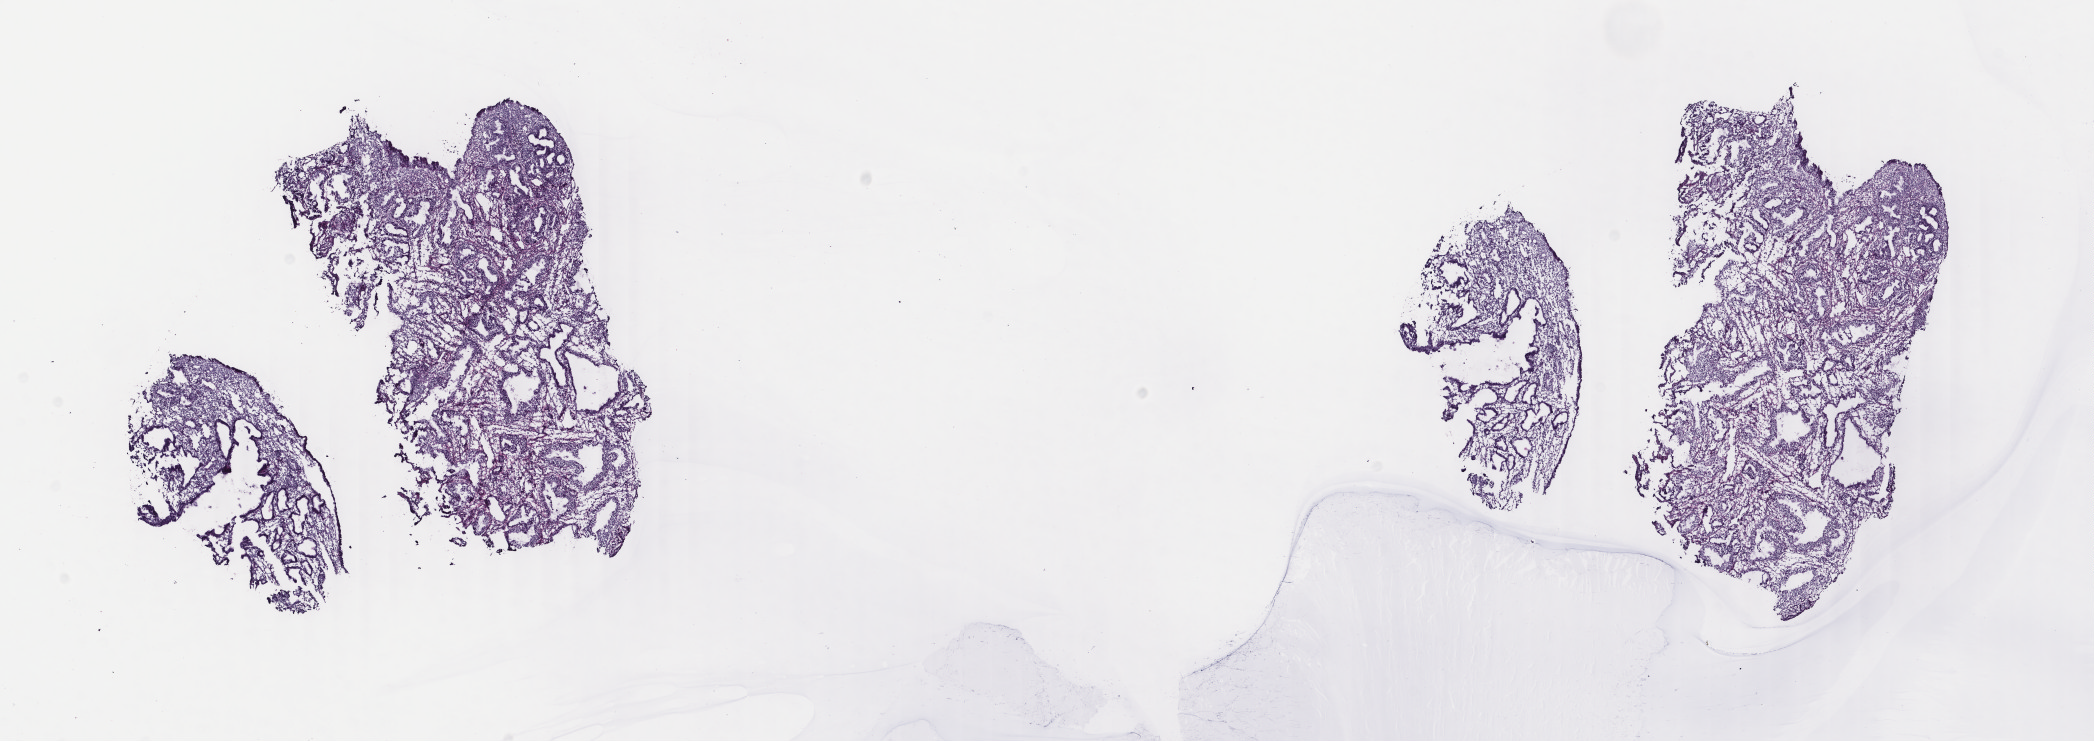
Digitized Hematoxylin and eosin (H&E) stained tissue section (whole slide), whole scanned area (about 16.7 x 5.9 mm, acquisition: 40x scan) shown as a low-resolution overview, frozen section from the bottom of the tissue portion, primary tumour sample from the uterus. Female, age 43 years at initial diagnosis. Histologic grade: G1 (well differentiated). Composition of this section per pathologist review: tumour cells 50%, tumour nuclei 50%, normal cells 0%, stromal cells 50%, necrosis 0%. Infiltration values recorded for this section: lymphocyte infiltration 30%, monocyte infiltration 2%, neutrophil infiltration 0%.
- diagnosis: Endometrioid adenocarcinoma, NOS (endometrium)
- FIGO stage: IA